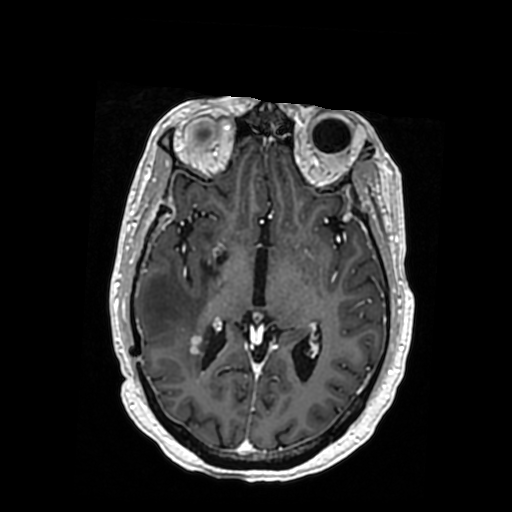
Brain MRI from a brain-tumour surgery series, one axial slice. Slice 193 of 364 in the series (ordered by position). T1-weighted post-contrast. 0.5 mm slice thickness. 512 × 512 image matrix, field of view 260 × 260 mm. From the clinical record (not read from this slice): histopathology: Oligodendroglioma; WHO grade: 3; IDH mutation: yes.
Annotated regions visible in this slice (expert manual segmentation):
- previous resection cavity: box from (x=216, y=254) to (x=226, y=266) px
- tumour: (x=163, y=333)–(x=173, y=350)